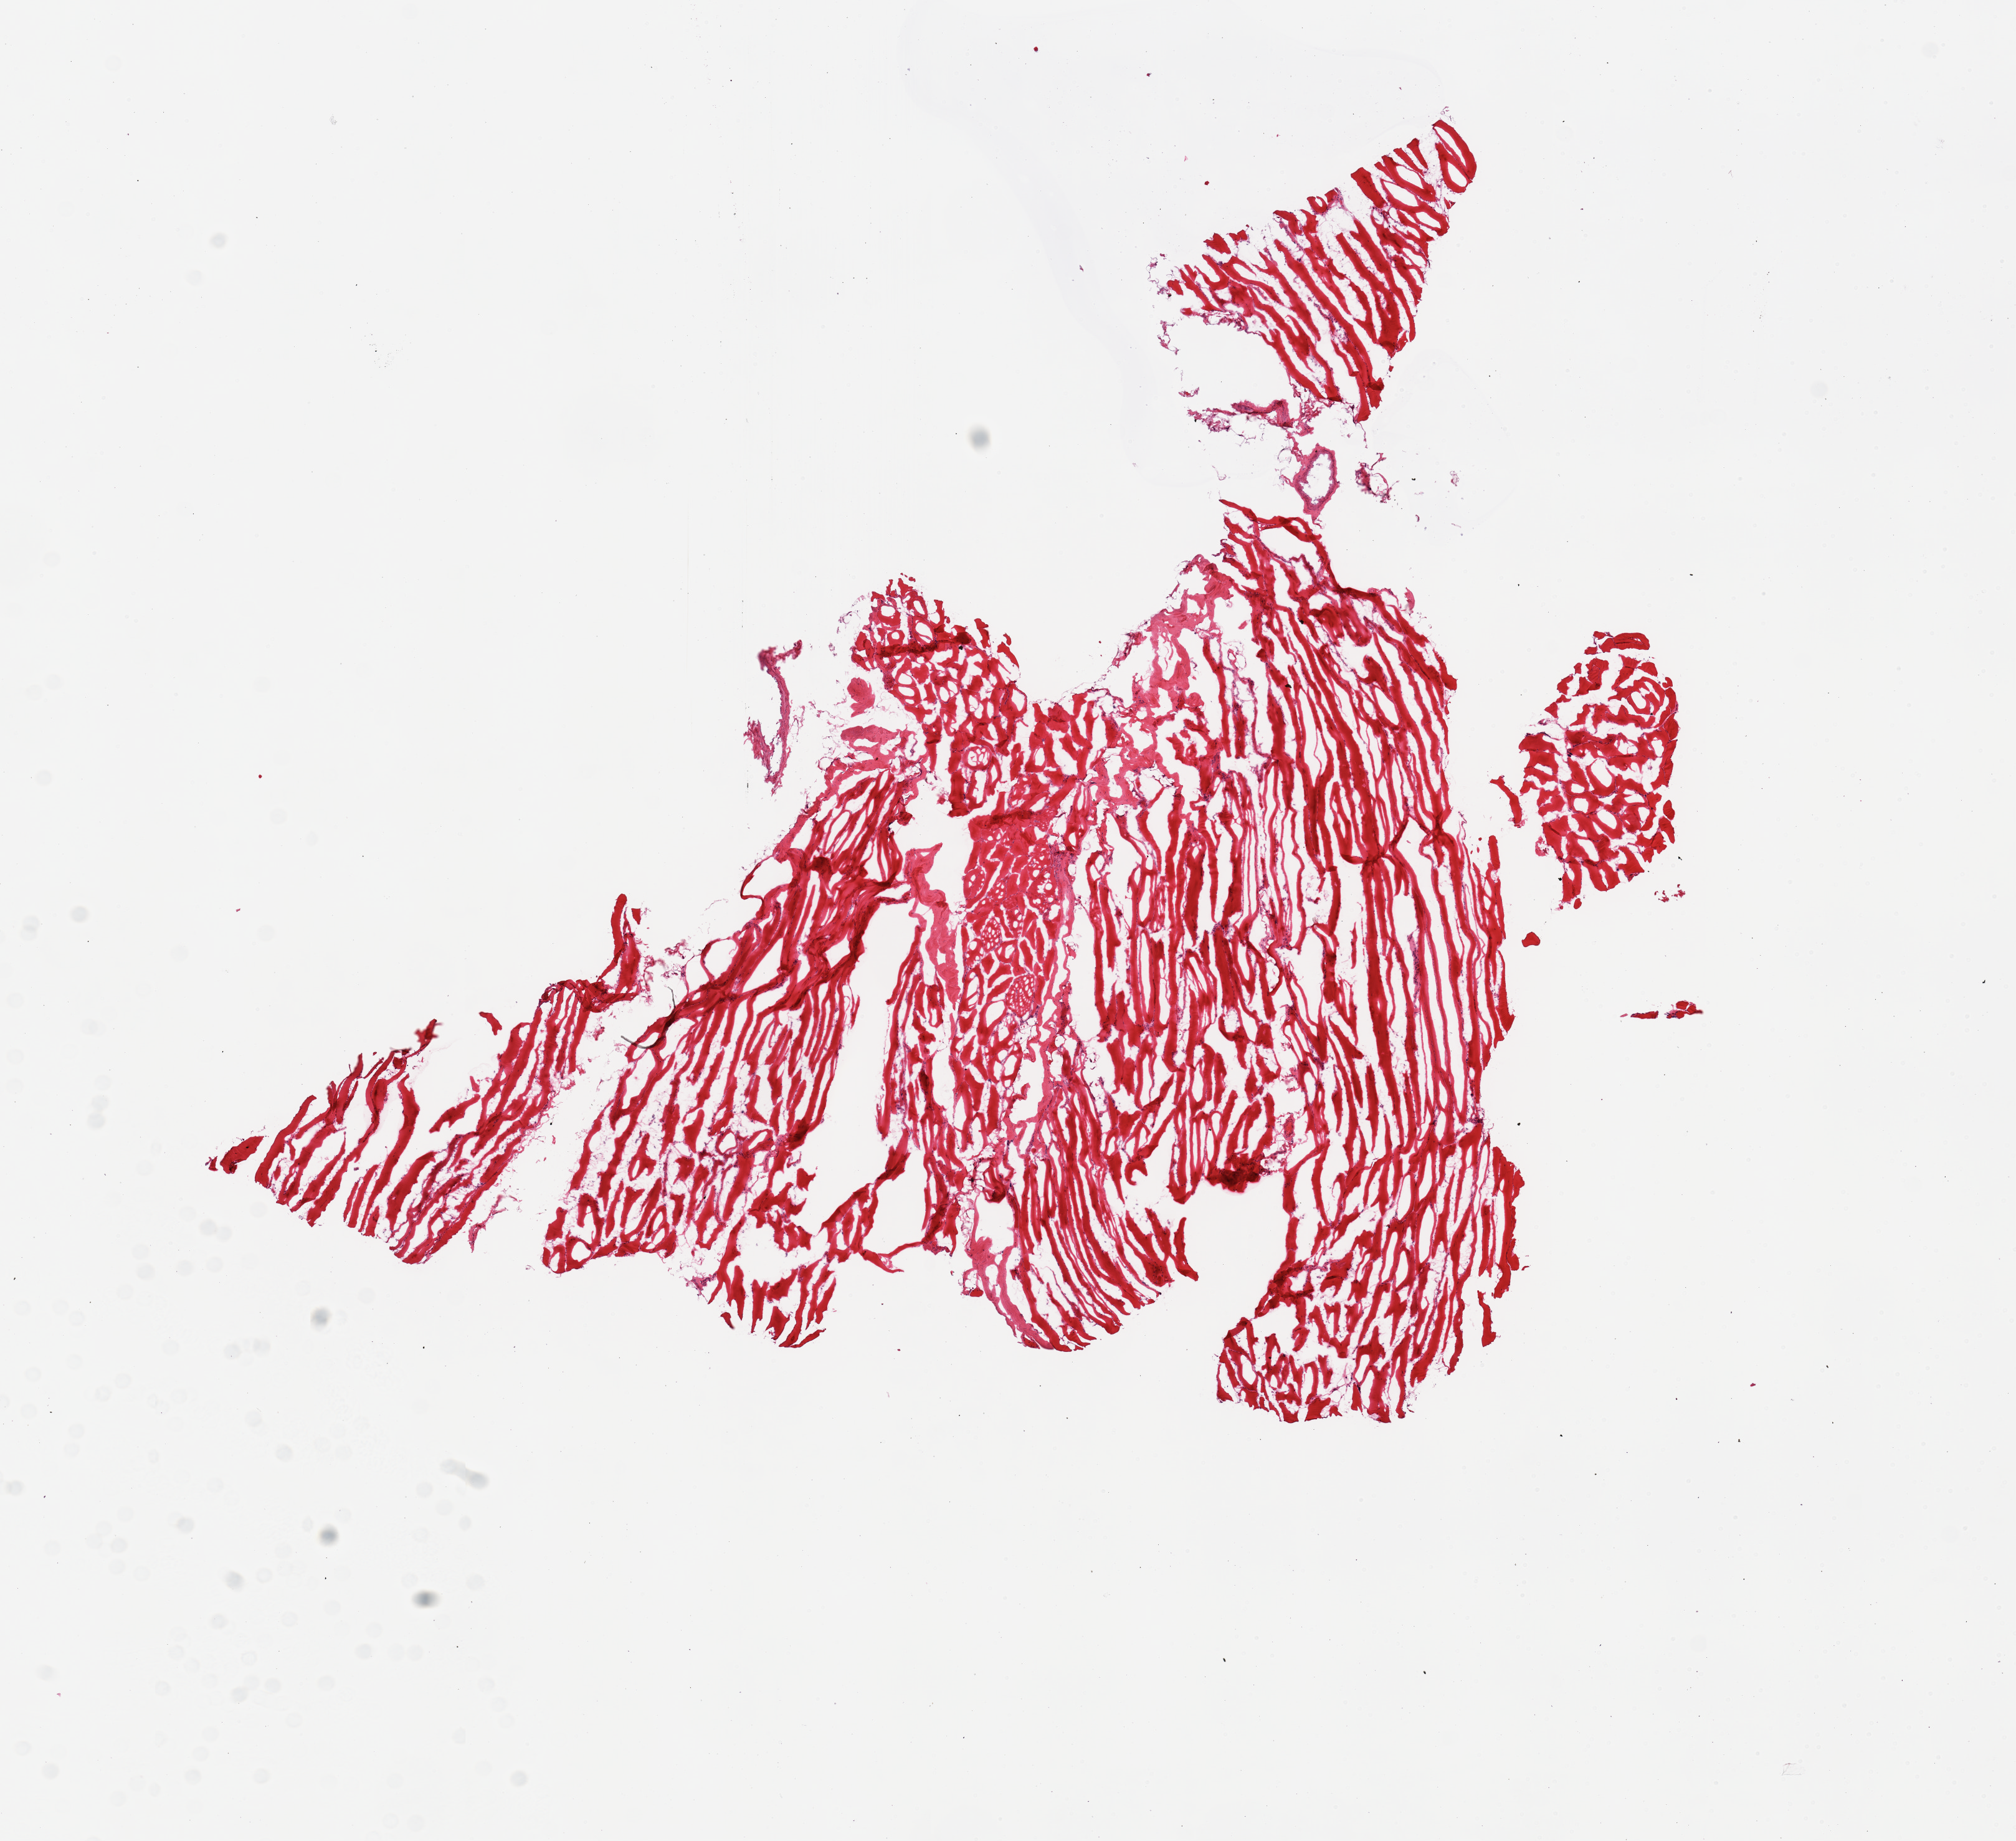
Digitized haematoxylin and eosin-stained section — whole scanned area (about 12.8 x 11.7 mm, acquisition: 20x scan) shown as a low-resolution overview. Frozen section. Target tissue: skeletal muscle. Tissue donor sample. Donor: male.
Reviewer comment on this tissue sample: 1 piece.